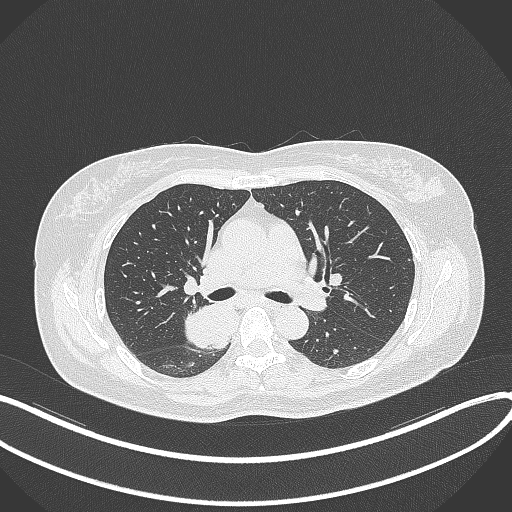
Chest CT, one axial slice. Position 224 of 331 along the scan axis. 120 kVp. Lung window (W 1500 / L -600 HU). 1 mm slice thickness. 512 × 512 image matrix, field of view 400 × 400 mm. Patient: female, 54 years. From the clinical record (not read from this slice): clinical TNM (as recorded): T4 N0 M0.
Structures marked on this image (bounding box drawn by a radiologist):
- lung tumour (recorded histology: adenocarcinoma): box from (x=183, y=299) to (x=240, y=351) px